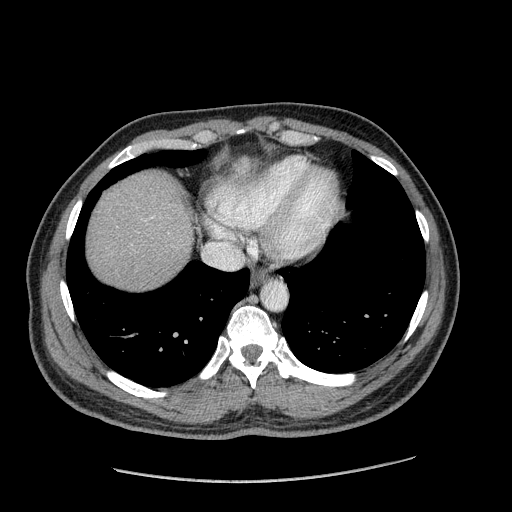
Contrast-enhanced abdominal CT (liver protocol), one axial slice. 120 kVp. Soft-tissue window (W 400 / L 40 HU). 2.5 mm slice thickness. 512 × 512 image matrix. From the clinical record (not read from this slice): diagnosis: hepatocellular carcinoma (patient treated with transarterial chemoembolisation; whether this scan precedes or follows treatment is not stated here); TNM stage (as recorded): Stage-I; Child-Pugh class: A; tumour differentiation: well differentiated; tumour nodularity: uninodular.
Outlined on this slice (semi-automatic segmentation, software-assisted and operator-edited):
- abdominal aorta: bounding box <260,281,287,311> (left, top, right, bottom; pixels)
- liver parenchyma outside the tumour (the mass and vessels are separate outlines, so this box may not span the whole liver): <86,172,192,290>